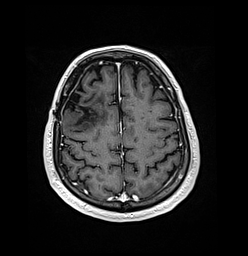
Brain MRI from a brain-tumour surgery series, one axial slice. Position 44 of 176 along the scan axis. T1-weighted post-contrast. 248 × 256 image matrix, field of view 242 × 250 mm. From the clinical record (not read from this slice): histopathology: Oligodendroglioma; WHO grade: 3; IDH mutation: yes; tumour location: Right Frontal.
Annotated regions visible in this slice (outlined manually by an expert reader):
- previous resection cavity: box from (x=64, y=90) to (x=90, y=122) px